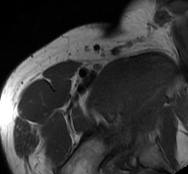
MRI of an extremity soft-tissue mass, one axial slice; slice 72 of 93 in the series (ordered by position); MR volume resampled by the dataset authors to the PET/CT grid (not the native acquisition matrix); 3.27 mm slice thickness; 188 × 174 image matrix. Male patient. Case-level facts recorded for this patient, not image findings: histological type: undifferentiated - pleiomorphic; grade: high; site of the primary tumour: right thigh.
Outlined on this slice (expert contour drawn on MRI and transferred to this co-registered scan by the dataset authors):
- gross tumour volume including surrounding oedema: bounding box <116,58,174,118> (left, top, right, bottom; pixels)
- gross tumour volume (mass): <116,65,167,113>